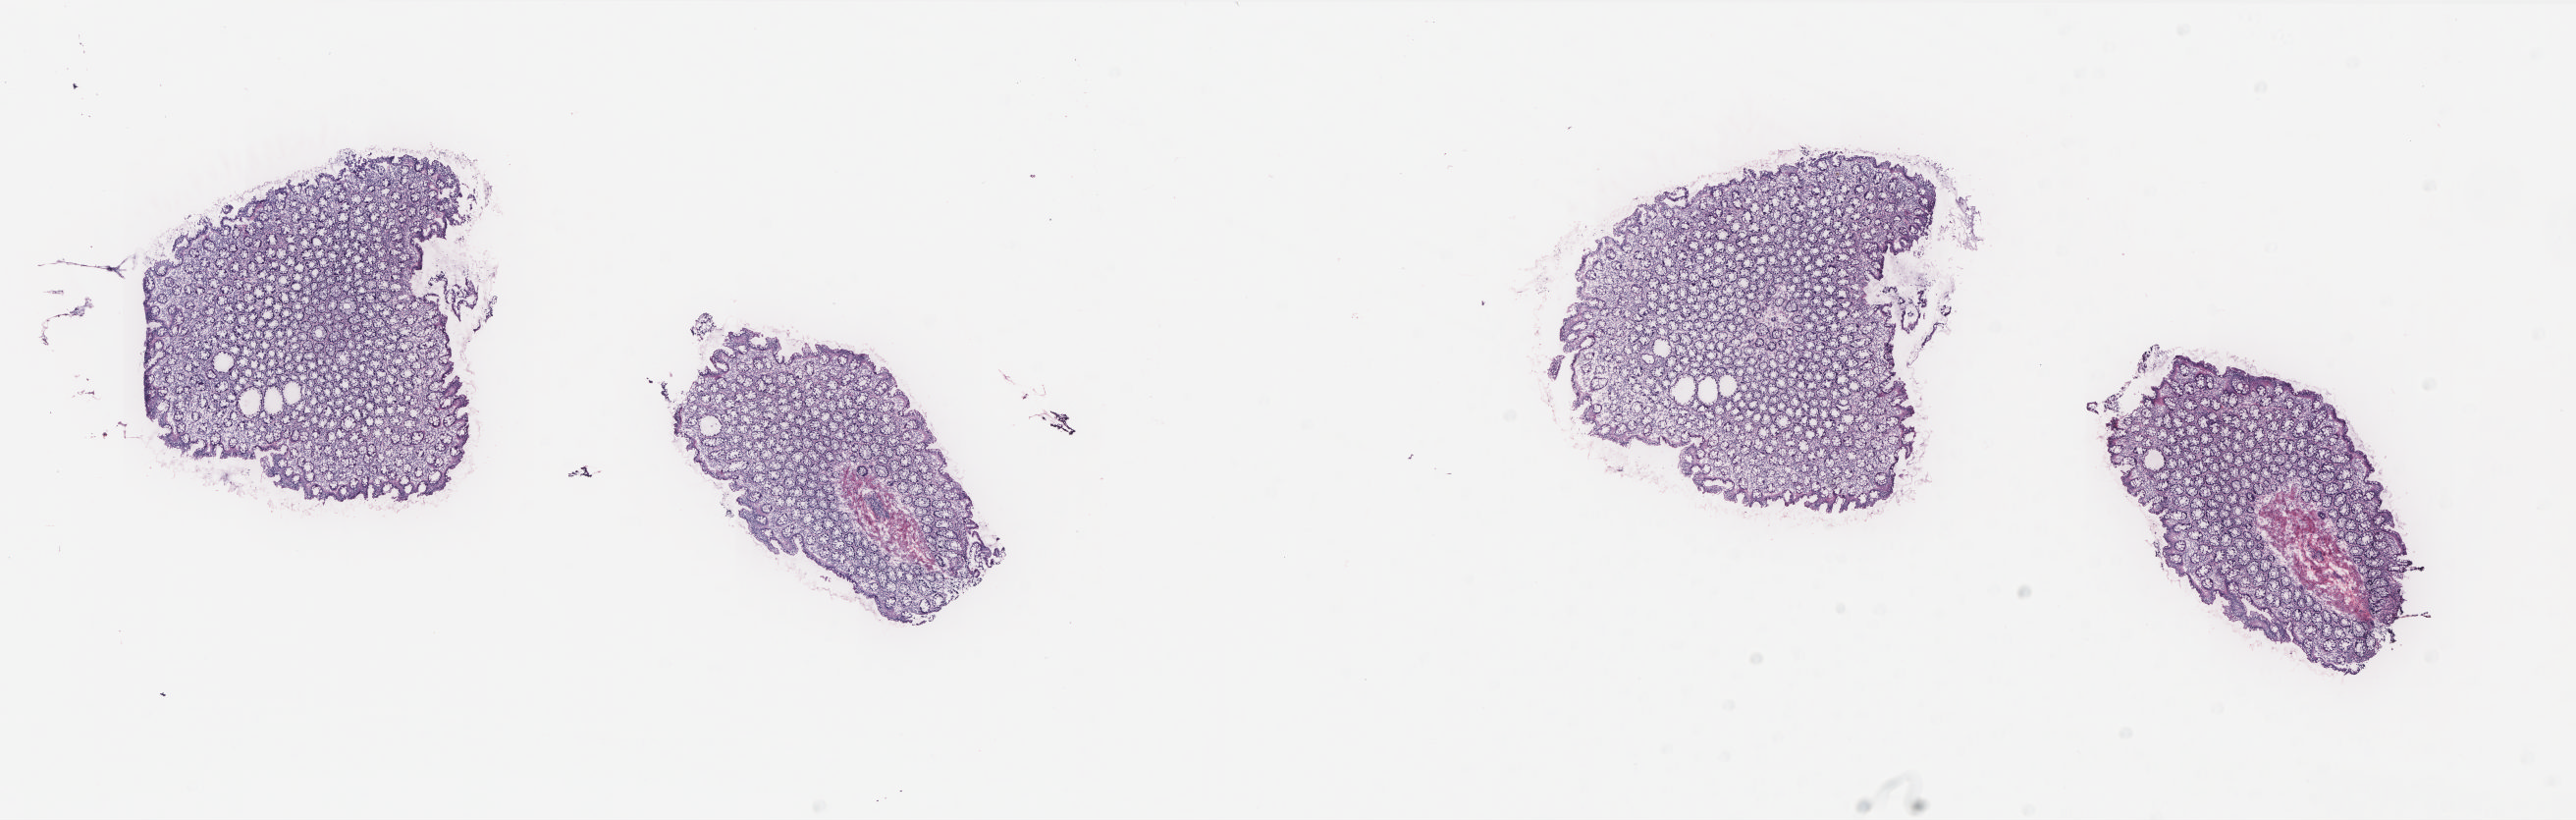
H&E-stained whole-slide image, low-resolution overview of the scanned area, about 21.0 x 6.7 mm. Frozen section from the top of the tissue portion. Colon, solid tissue normal (non-tumour tissue) sample. Patient: female, age at initial diagnosis 80 years. Pathologist review of this section (percent, as recorded): tumour cells 0%, normal cells 100%. Inflammatory infiltration, as recorded: lymphocyte infiltration 40%, monocyte infiltration 10%, neutrophil infiltration 0%.
• this section: solid tissue normal sample (biorepository sample class)
• patient diagnosis: Adenocarcinoma, NOS (sigmoid colon)